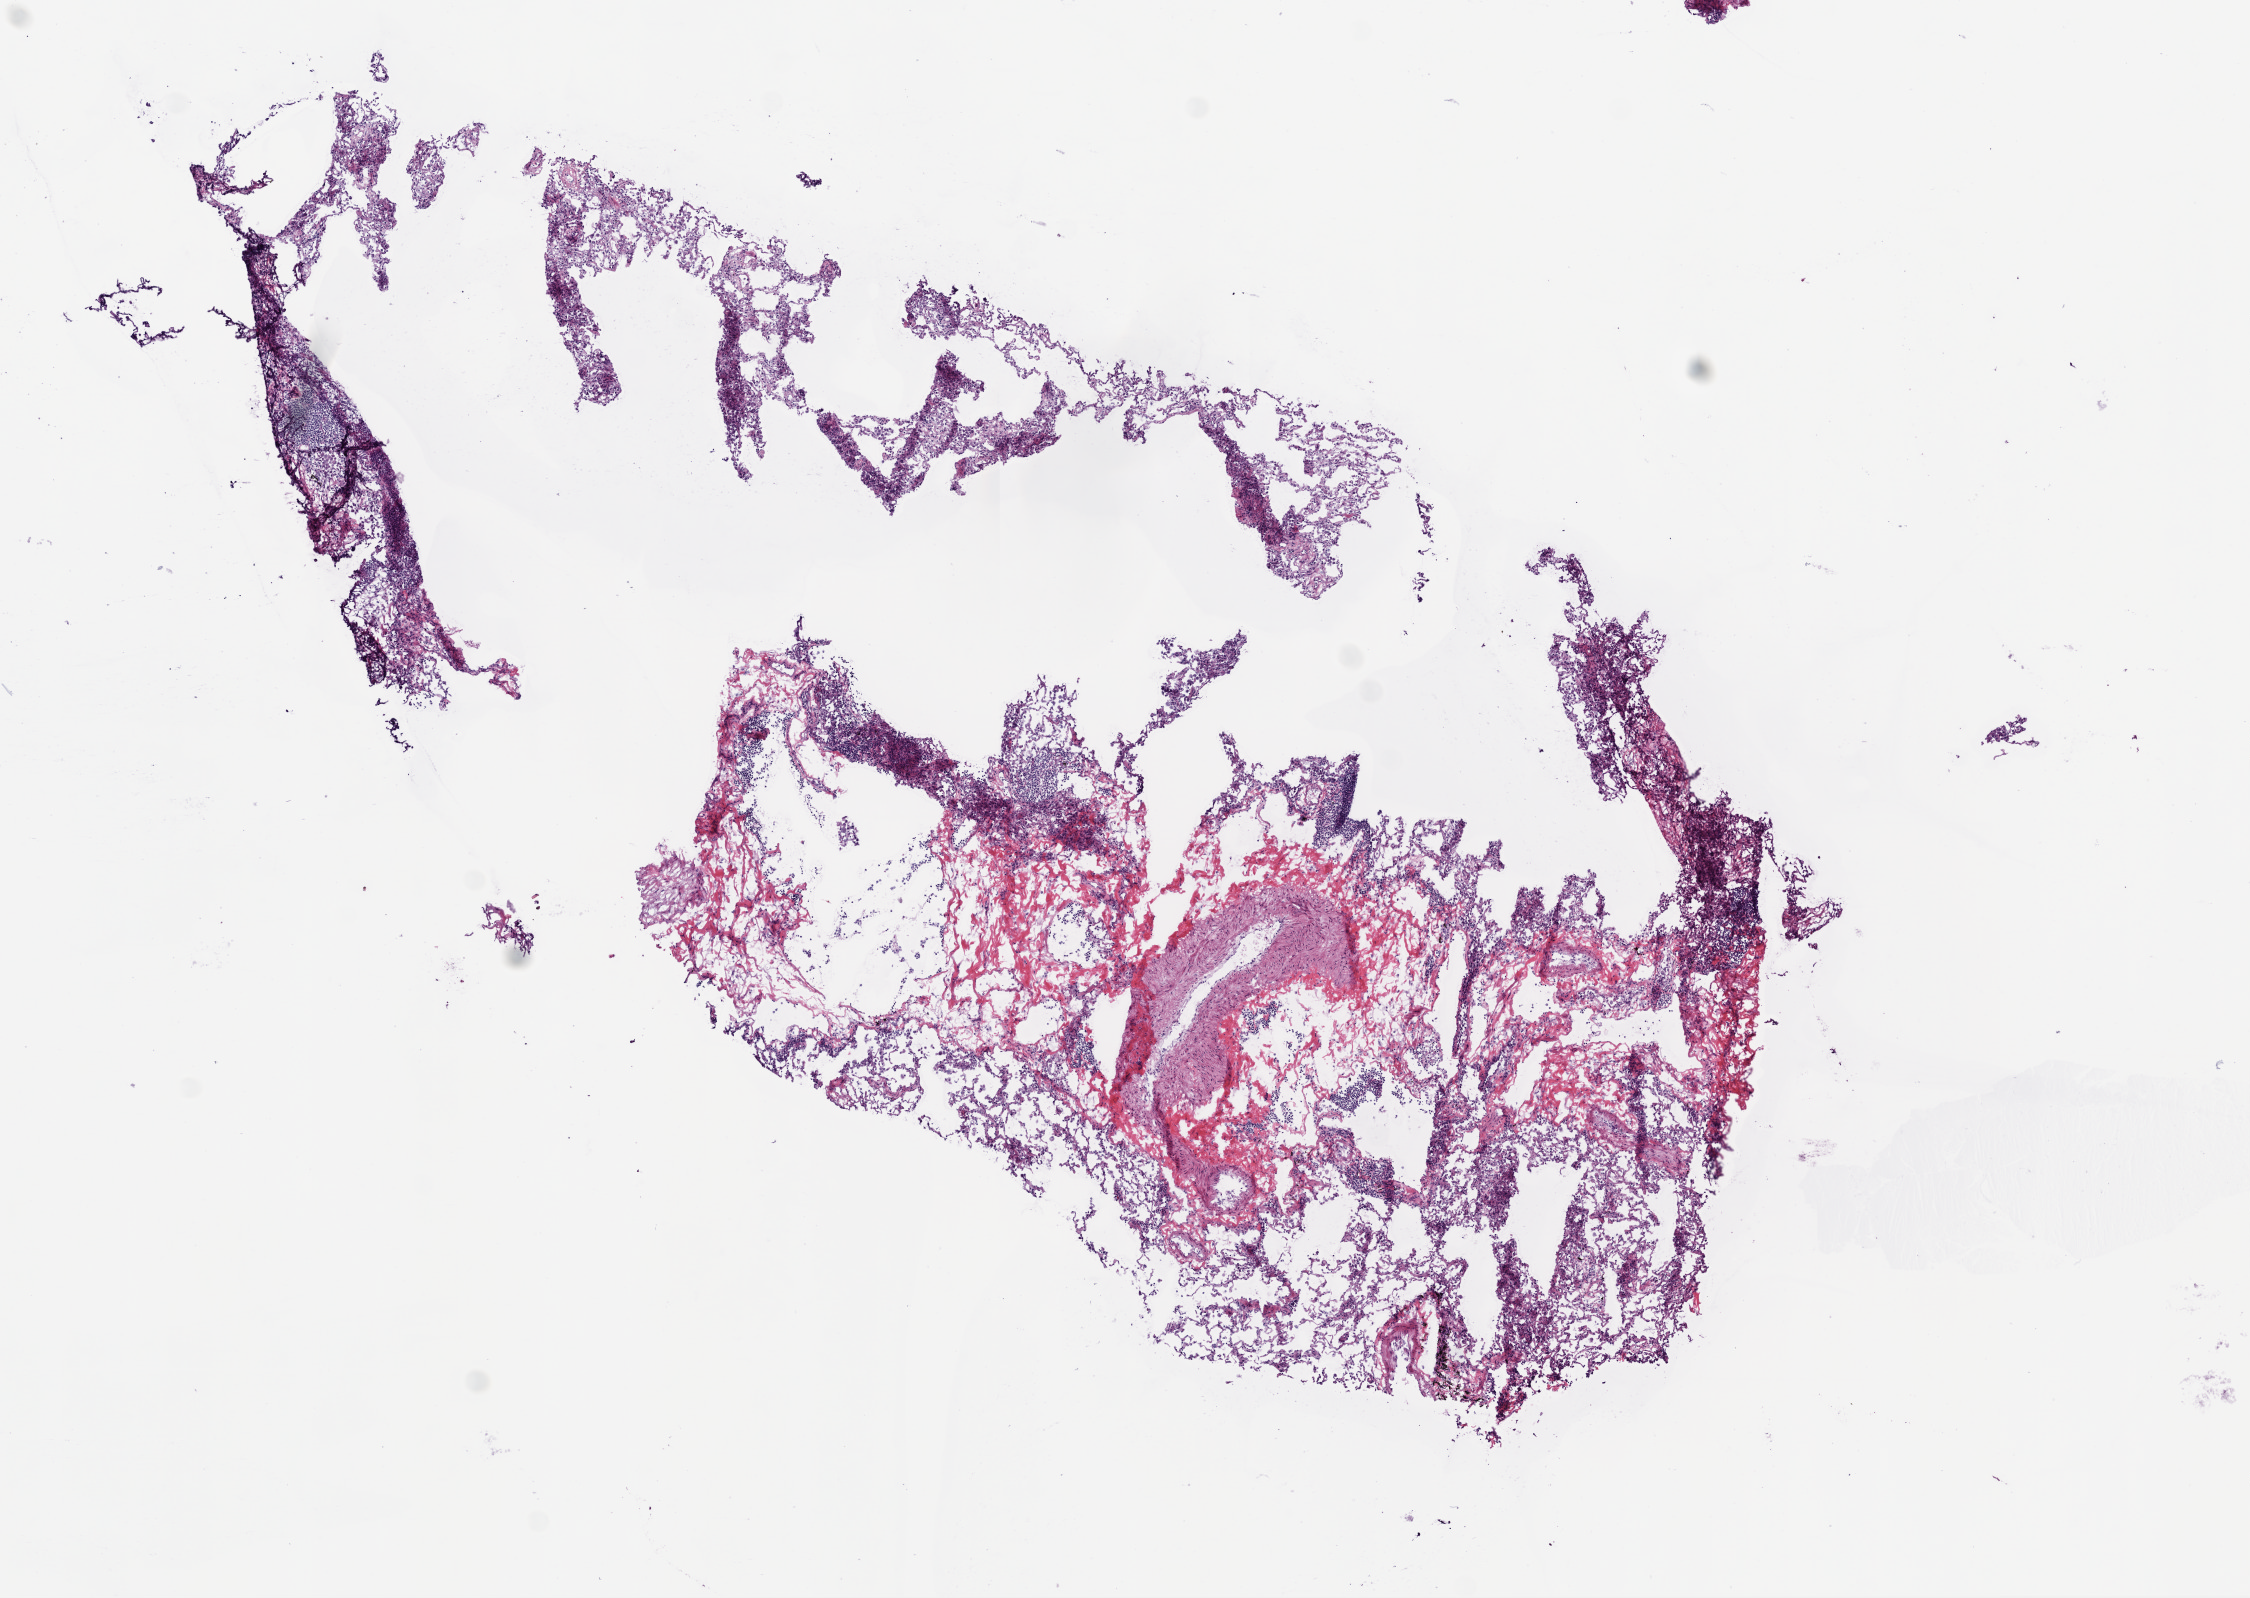
H&E-stained whole-slide image — a low-resolution overview of the entire scanned area, about 9.0 x 6.4 mm (slide scanned at 20x). Frozen section from the bottom of the tissue portion. Solid tissue normal (non-tumour tissue) sample from the lung. Male, age 52 years at initial diagnosis.
This section: solid tissue normal sample (biorepository sample class). Patient diagnosis: Squamous cell carcinoma, NOS (lower lobe, lung).